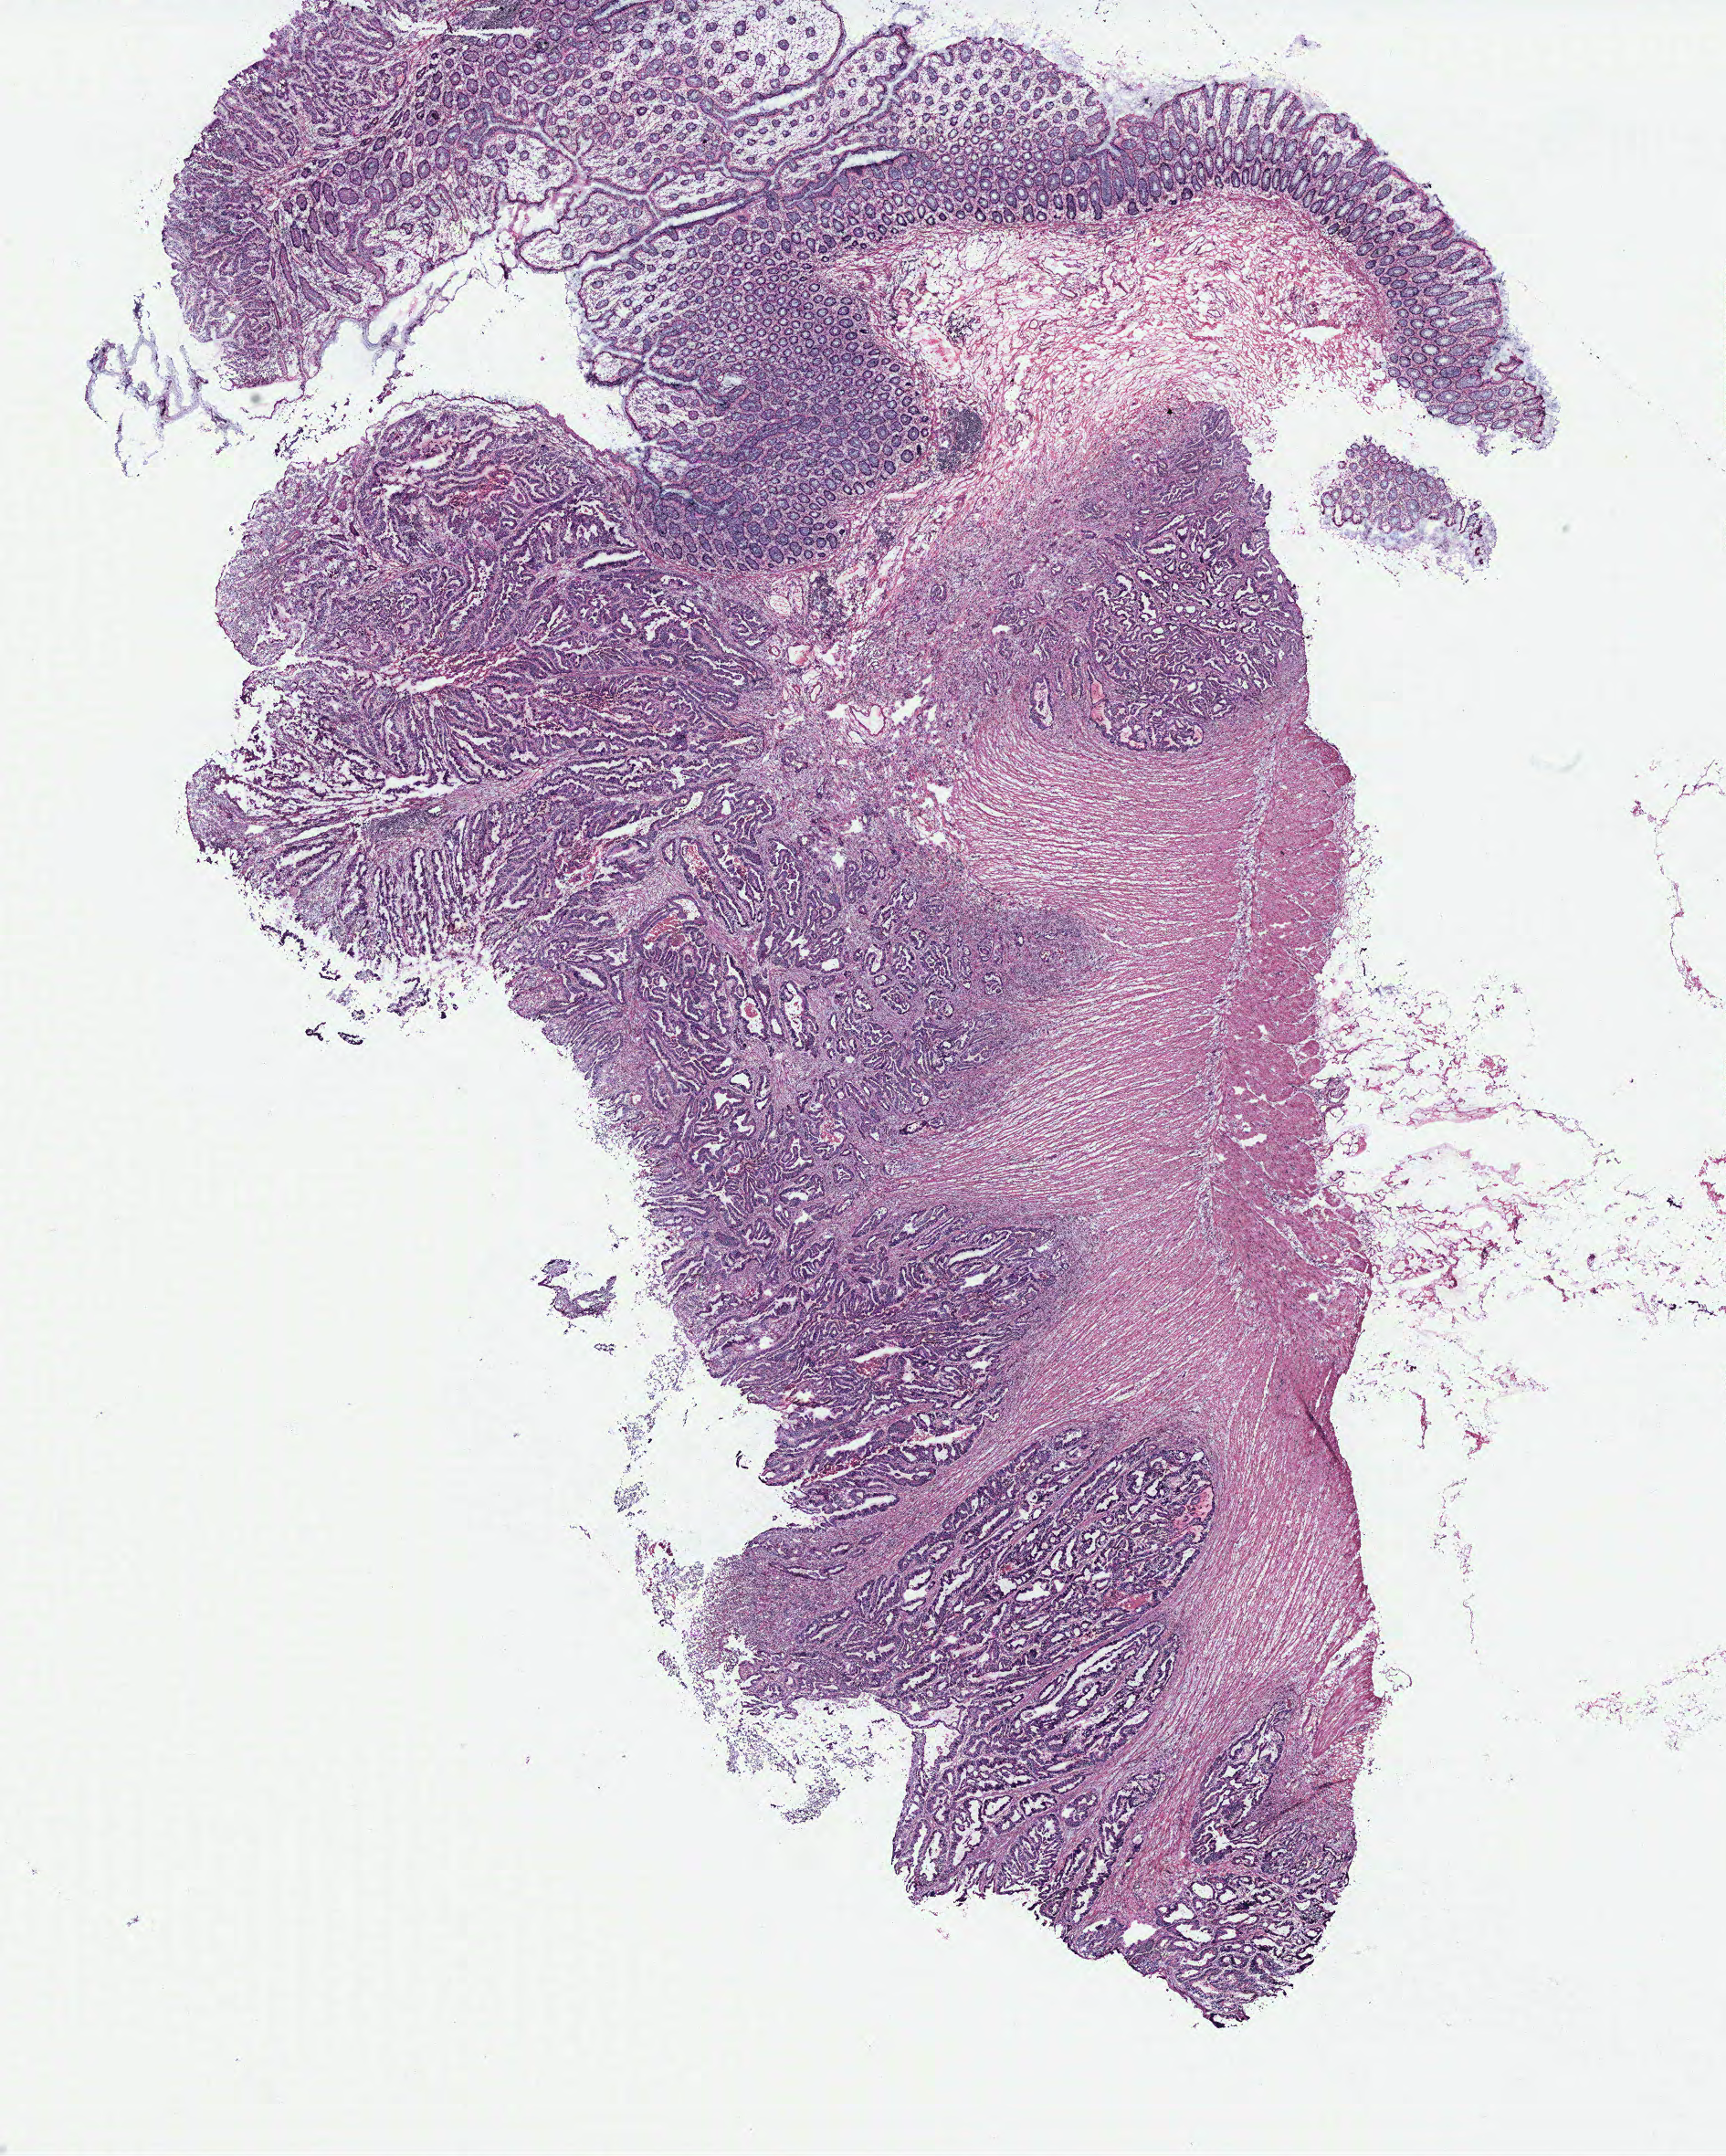
Digitized H&E-stained tissue section (whole slide), whole scanned area (about 15.1 x 18.9 mm, slide scanned at 40x) shown as a low-resolution overview. Colon, tissue type not recorded.
• patient diagnosis (cohort enrolment): colon cancer (colon)